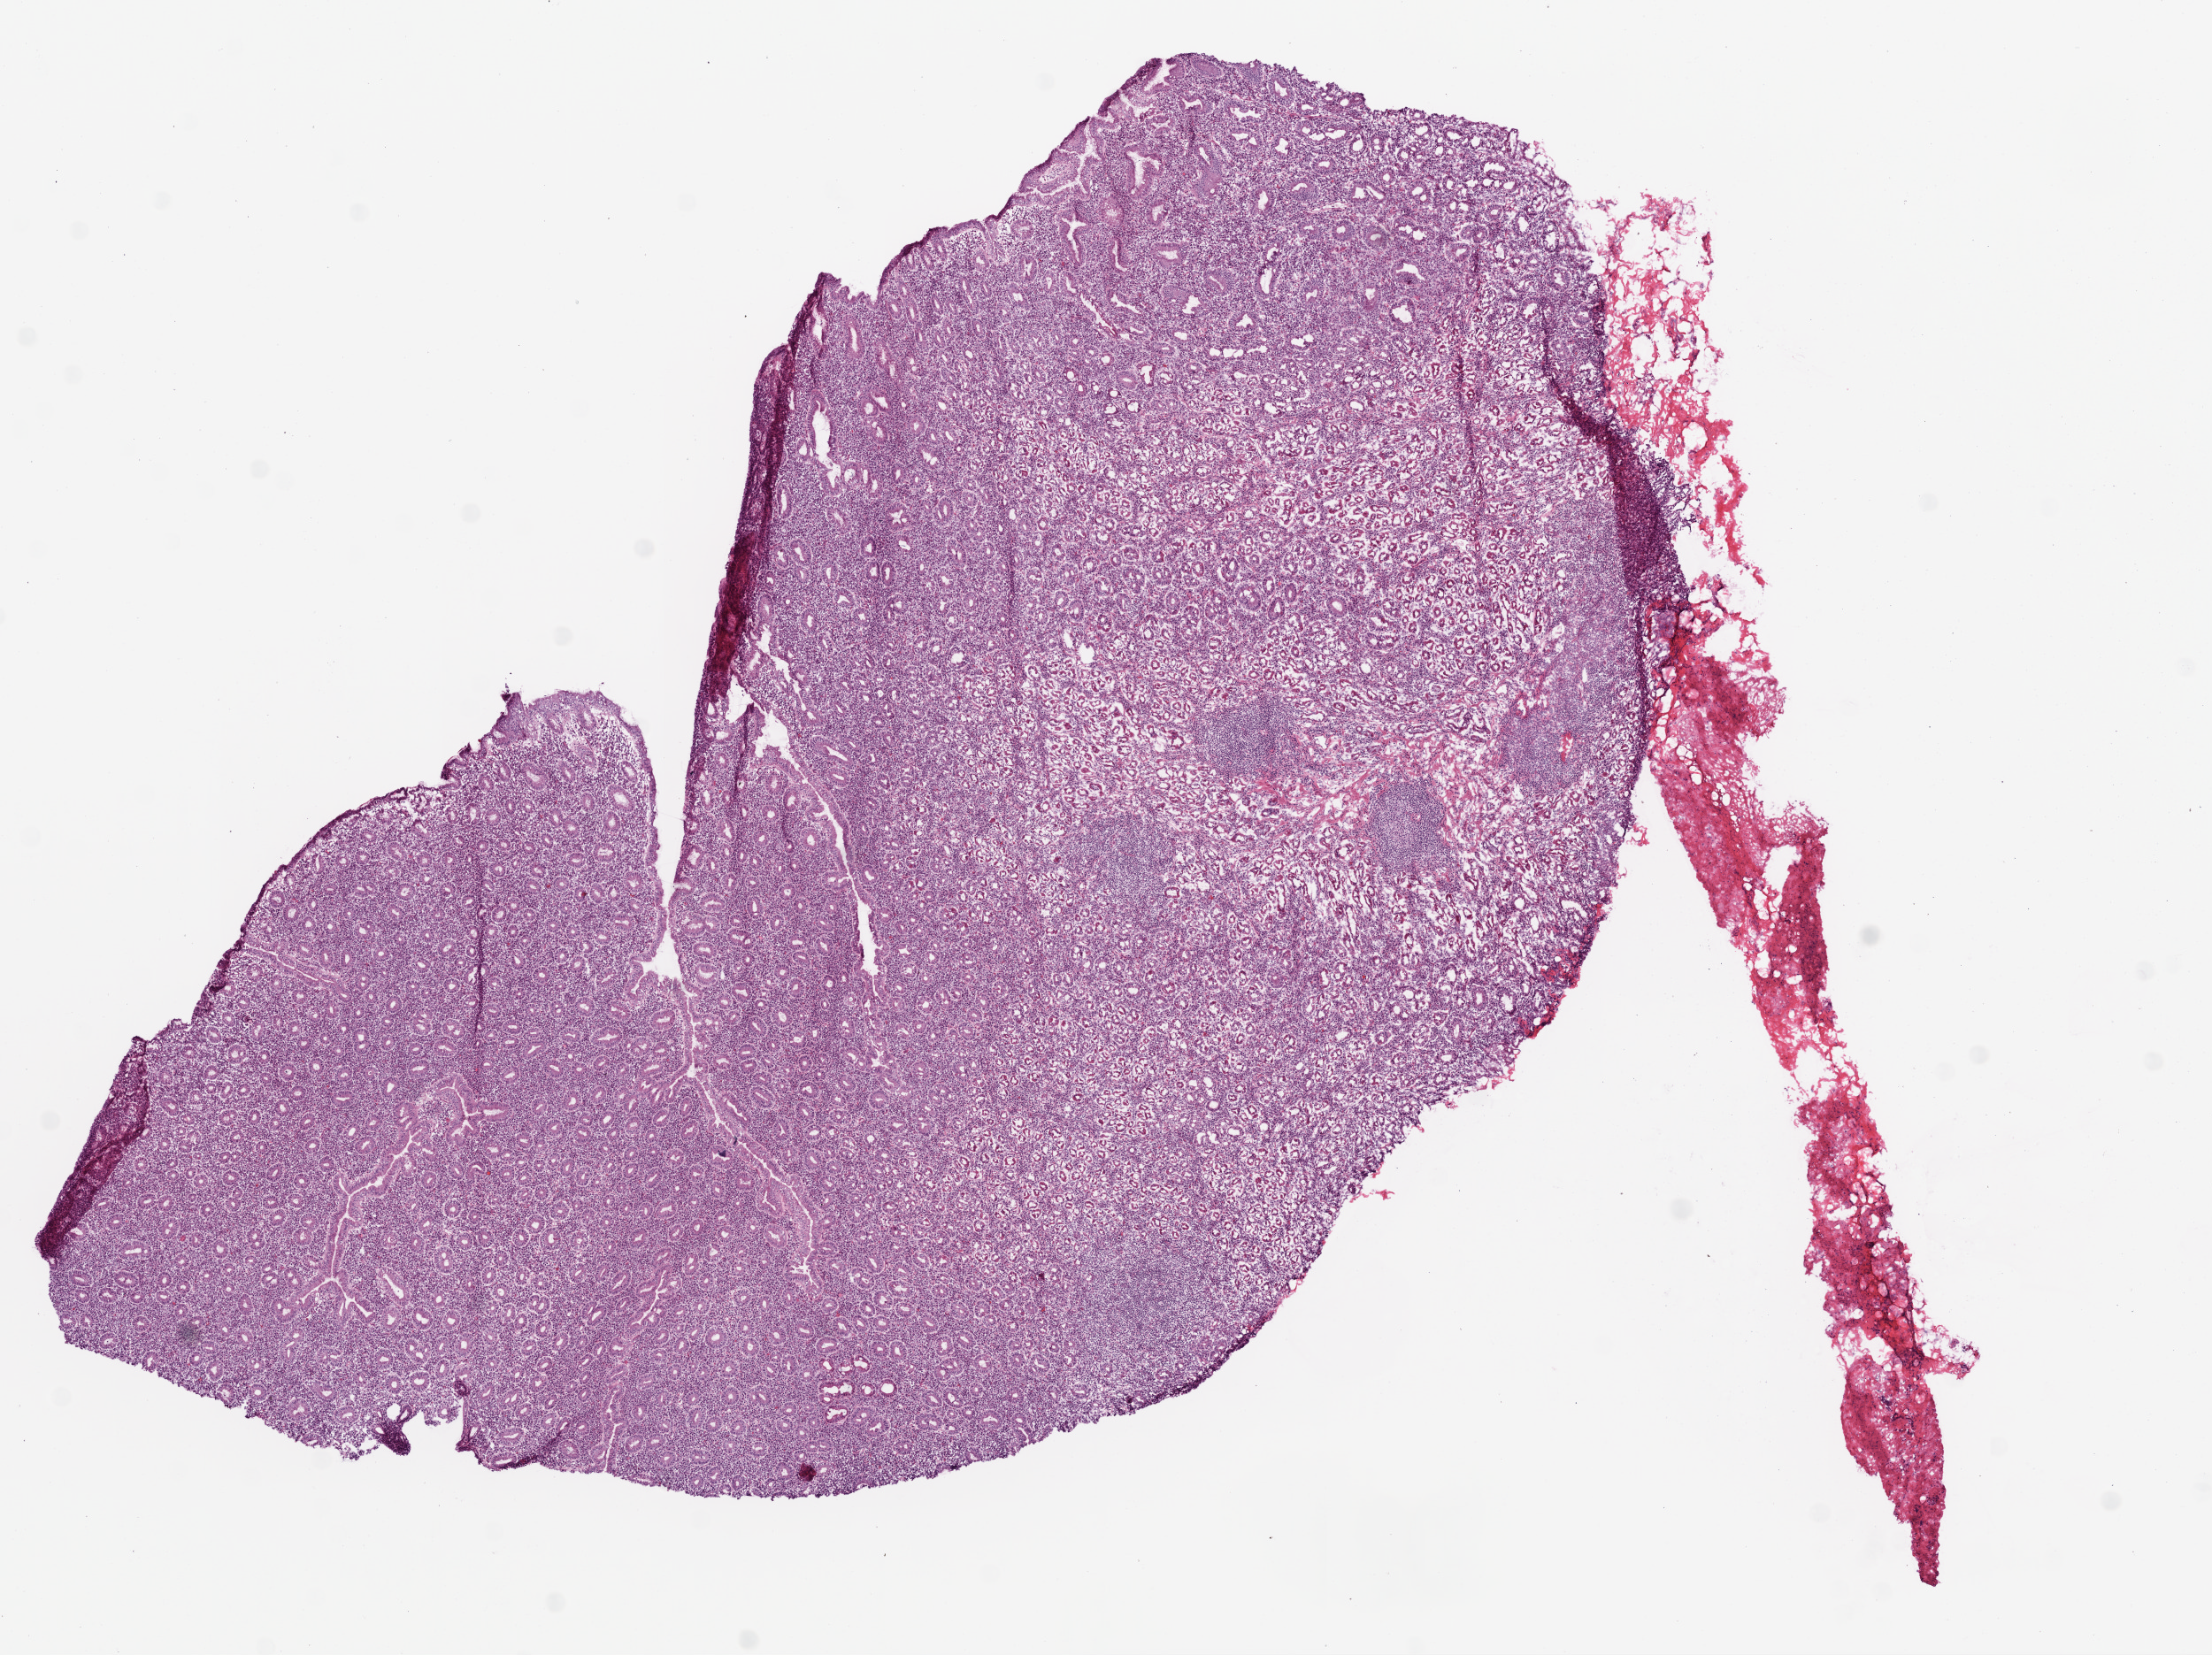
Digitized Hematoxylin and eosin (H&E) stained tissue section (whole slide), whole scanned area (about 10.0 x 7.5 mm, from a 20x scan) shown as a low-resolution overview; frozen section from the top of the tissue portion; solid tissue normal (non-tumour tissue) sample from the stomach. Male patient; age at initial diagnosis 51 years.
This section: solid tissue normal sample (biorepository sample class). Patient diagnosis: Adenocarcinoma, NOS.